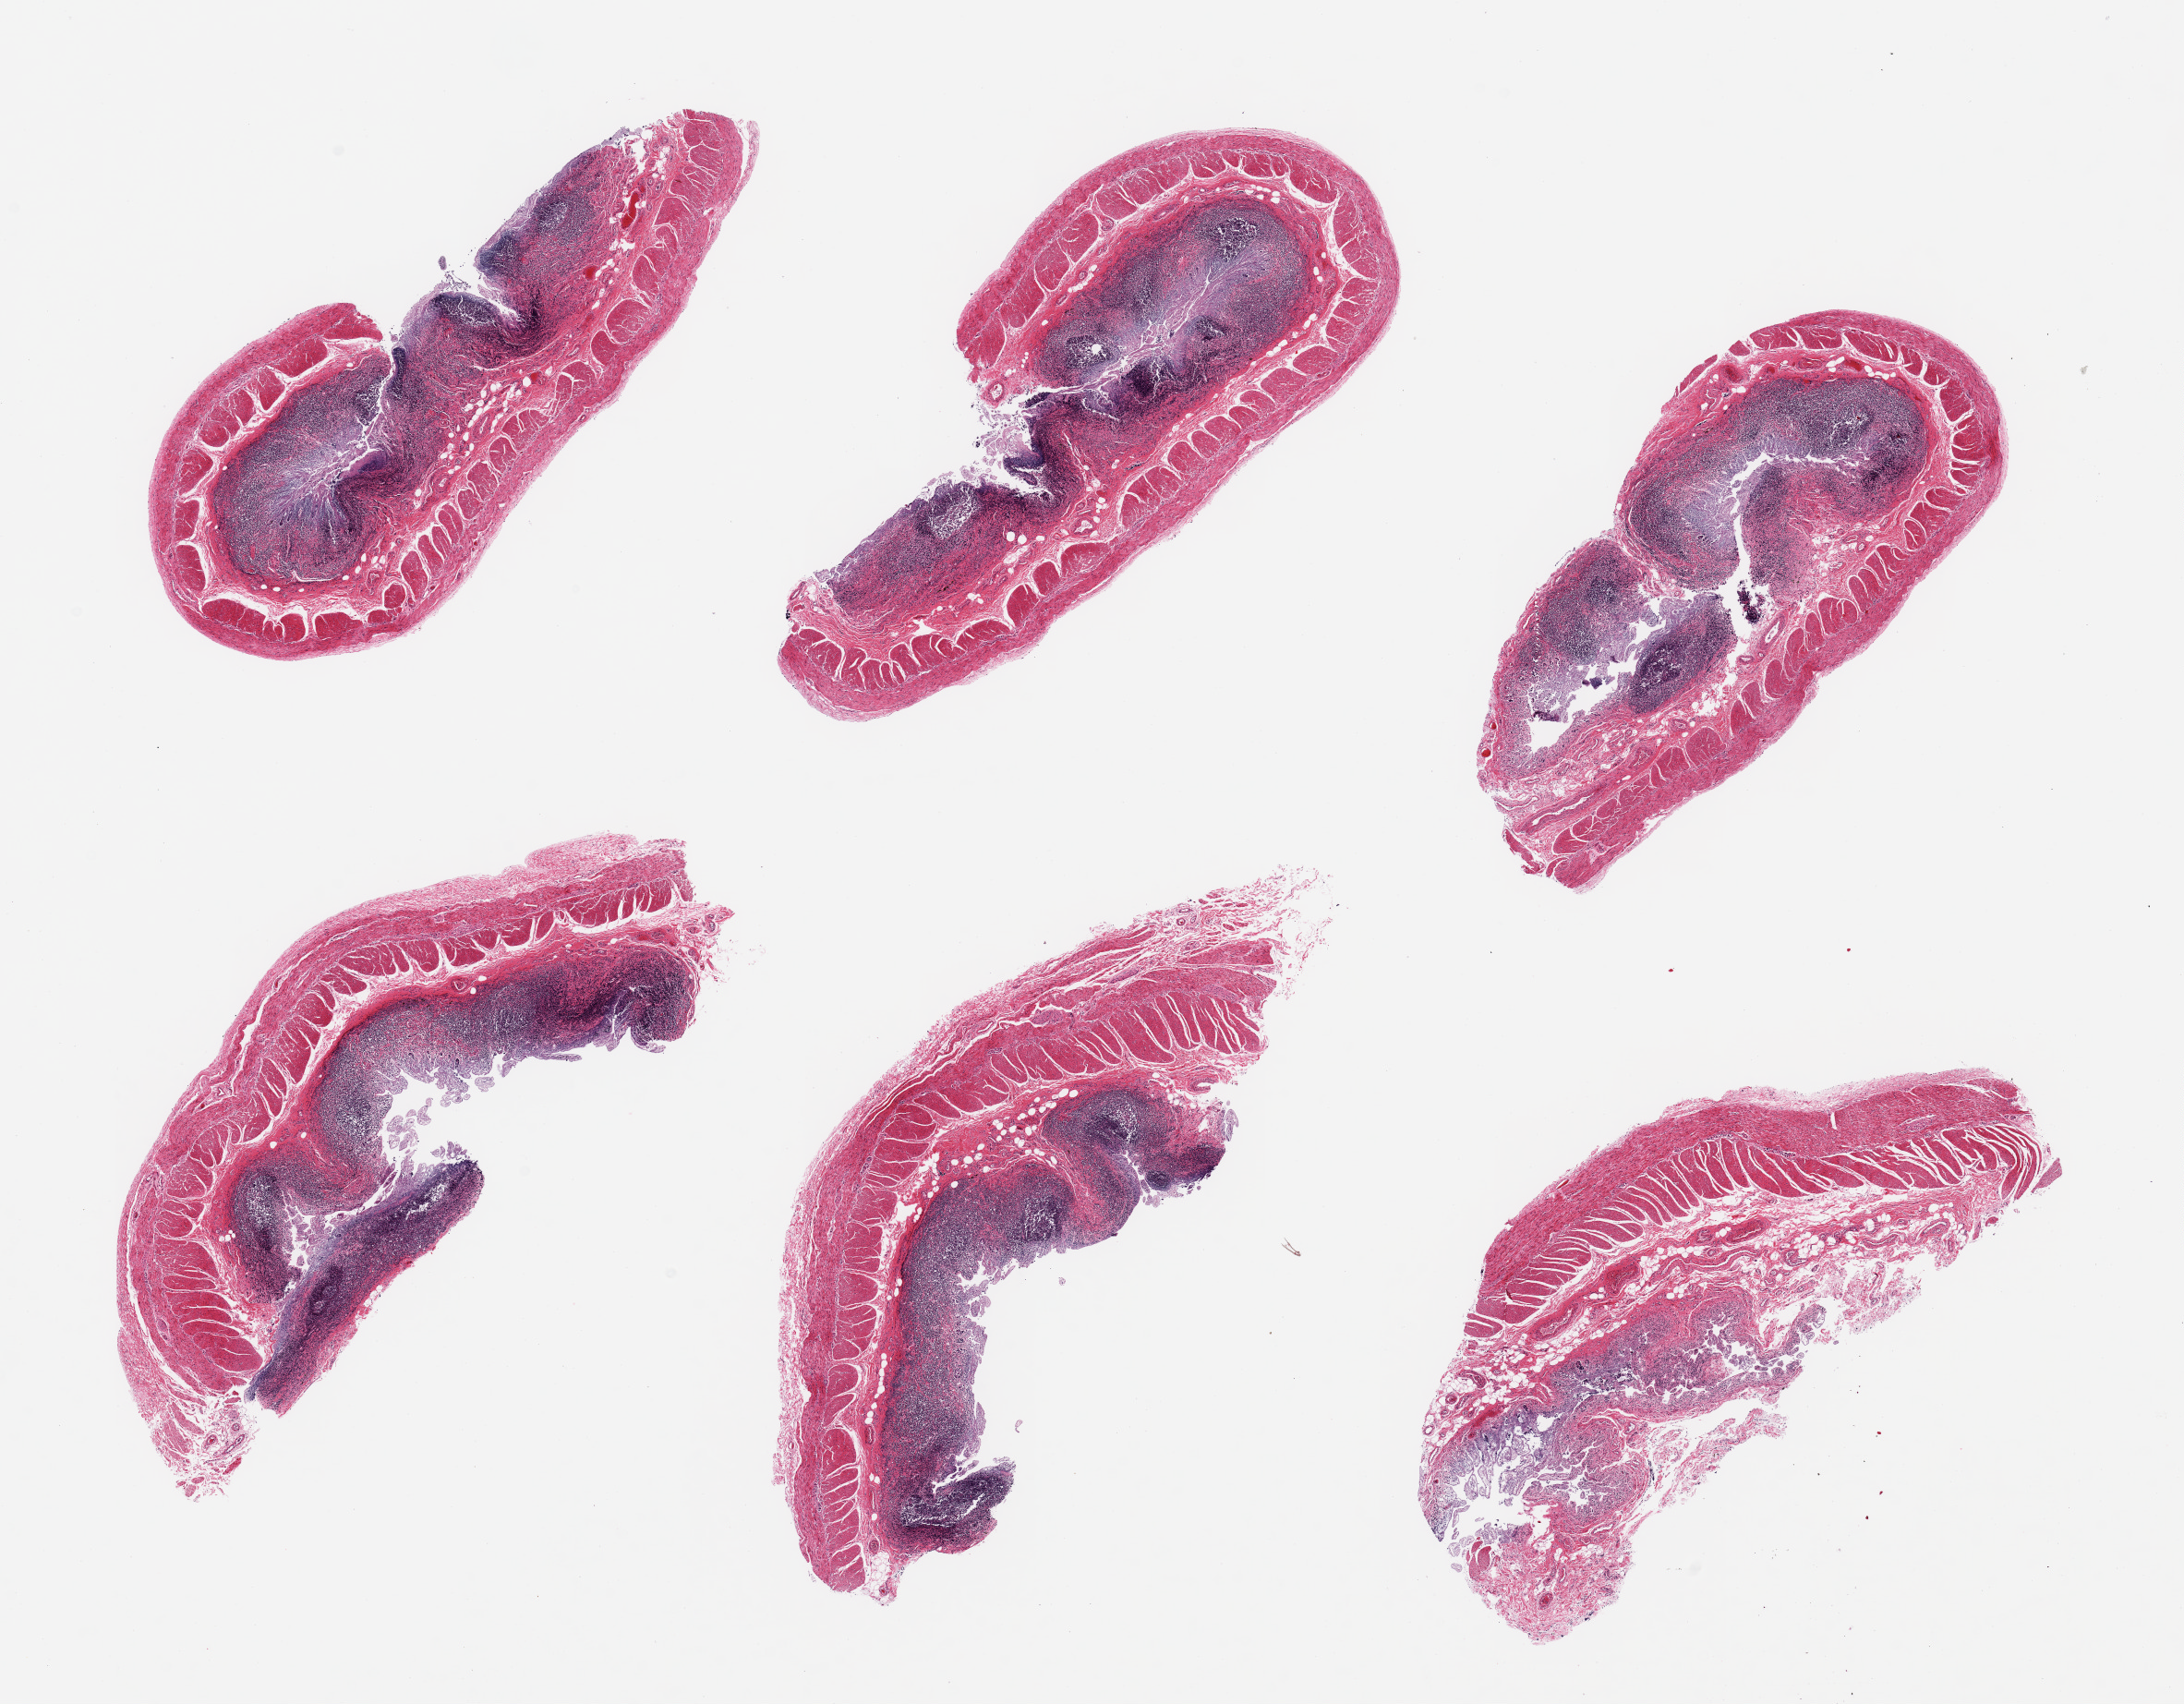
H&E whole-slide image, whole scanned area (about 18.7 x 14.6 mm) shown as a low-resolution overview.
Specimen: PAXgene-fixed paraffin-embedded (PFPE) section; sampled site (target tissue): ileum; tissue donor sample.